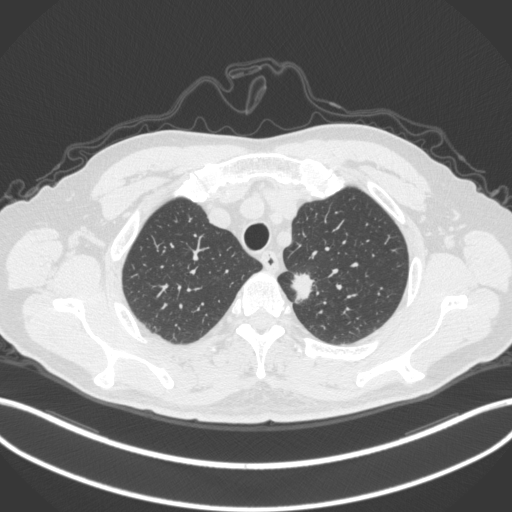
Chest CT, one axial slice. Slice 313 of 382 in the series (ordered by position). 120 kVp. Lung window (W 1500 / L -600 HU). 1 mm slice thickness. 512 × 512 image matrix, field of view 400 × 400 mm. Patient: male, 64 years. Case-level facts recorded for this patient, not image findings: clinical TNM (as recorded): T1c N0 M0.
Annotated regions visible in this slice (bounding box drawn by a radiologist):
- lung tumour (recorded histology: adenocarcinoma): bounding box [x1, y1, x2, y2] px = [289, 269, 318, 307]